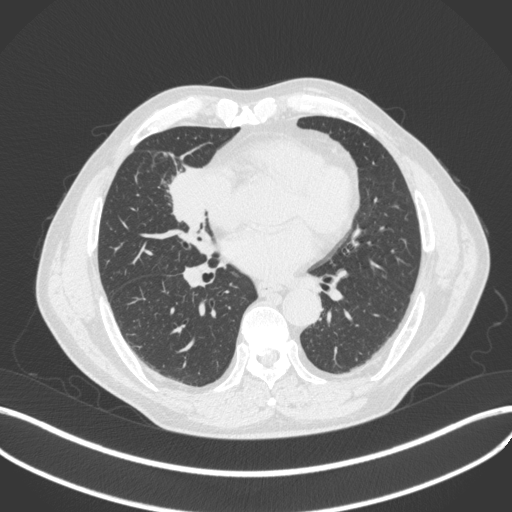
Chest CT, one axial slice; slice 183 of 429 in the series (ordered by position); reconstruction kernel B31f; lung window (W 1500 / L -600 HU); 1 mm slice thickness; 512 × 512 image matrix, field of view 400 × 400 mm. Male patient, age 61 years. From the clinical record (not read from this slice): clinical TNM (as recorded): T2b N1 M0.
Outlined on this slice (bounding box drawn by a radiologist):
- lung tumour (recorded histology: squamous cell carcinoma): bounding box [x1, y1, x2, y2] px = [164, 153, 212, 231]